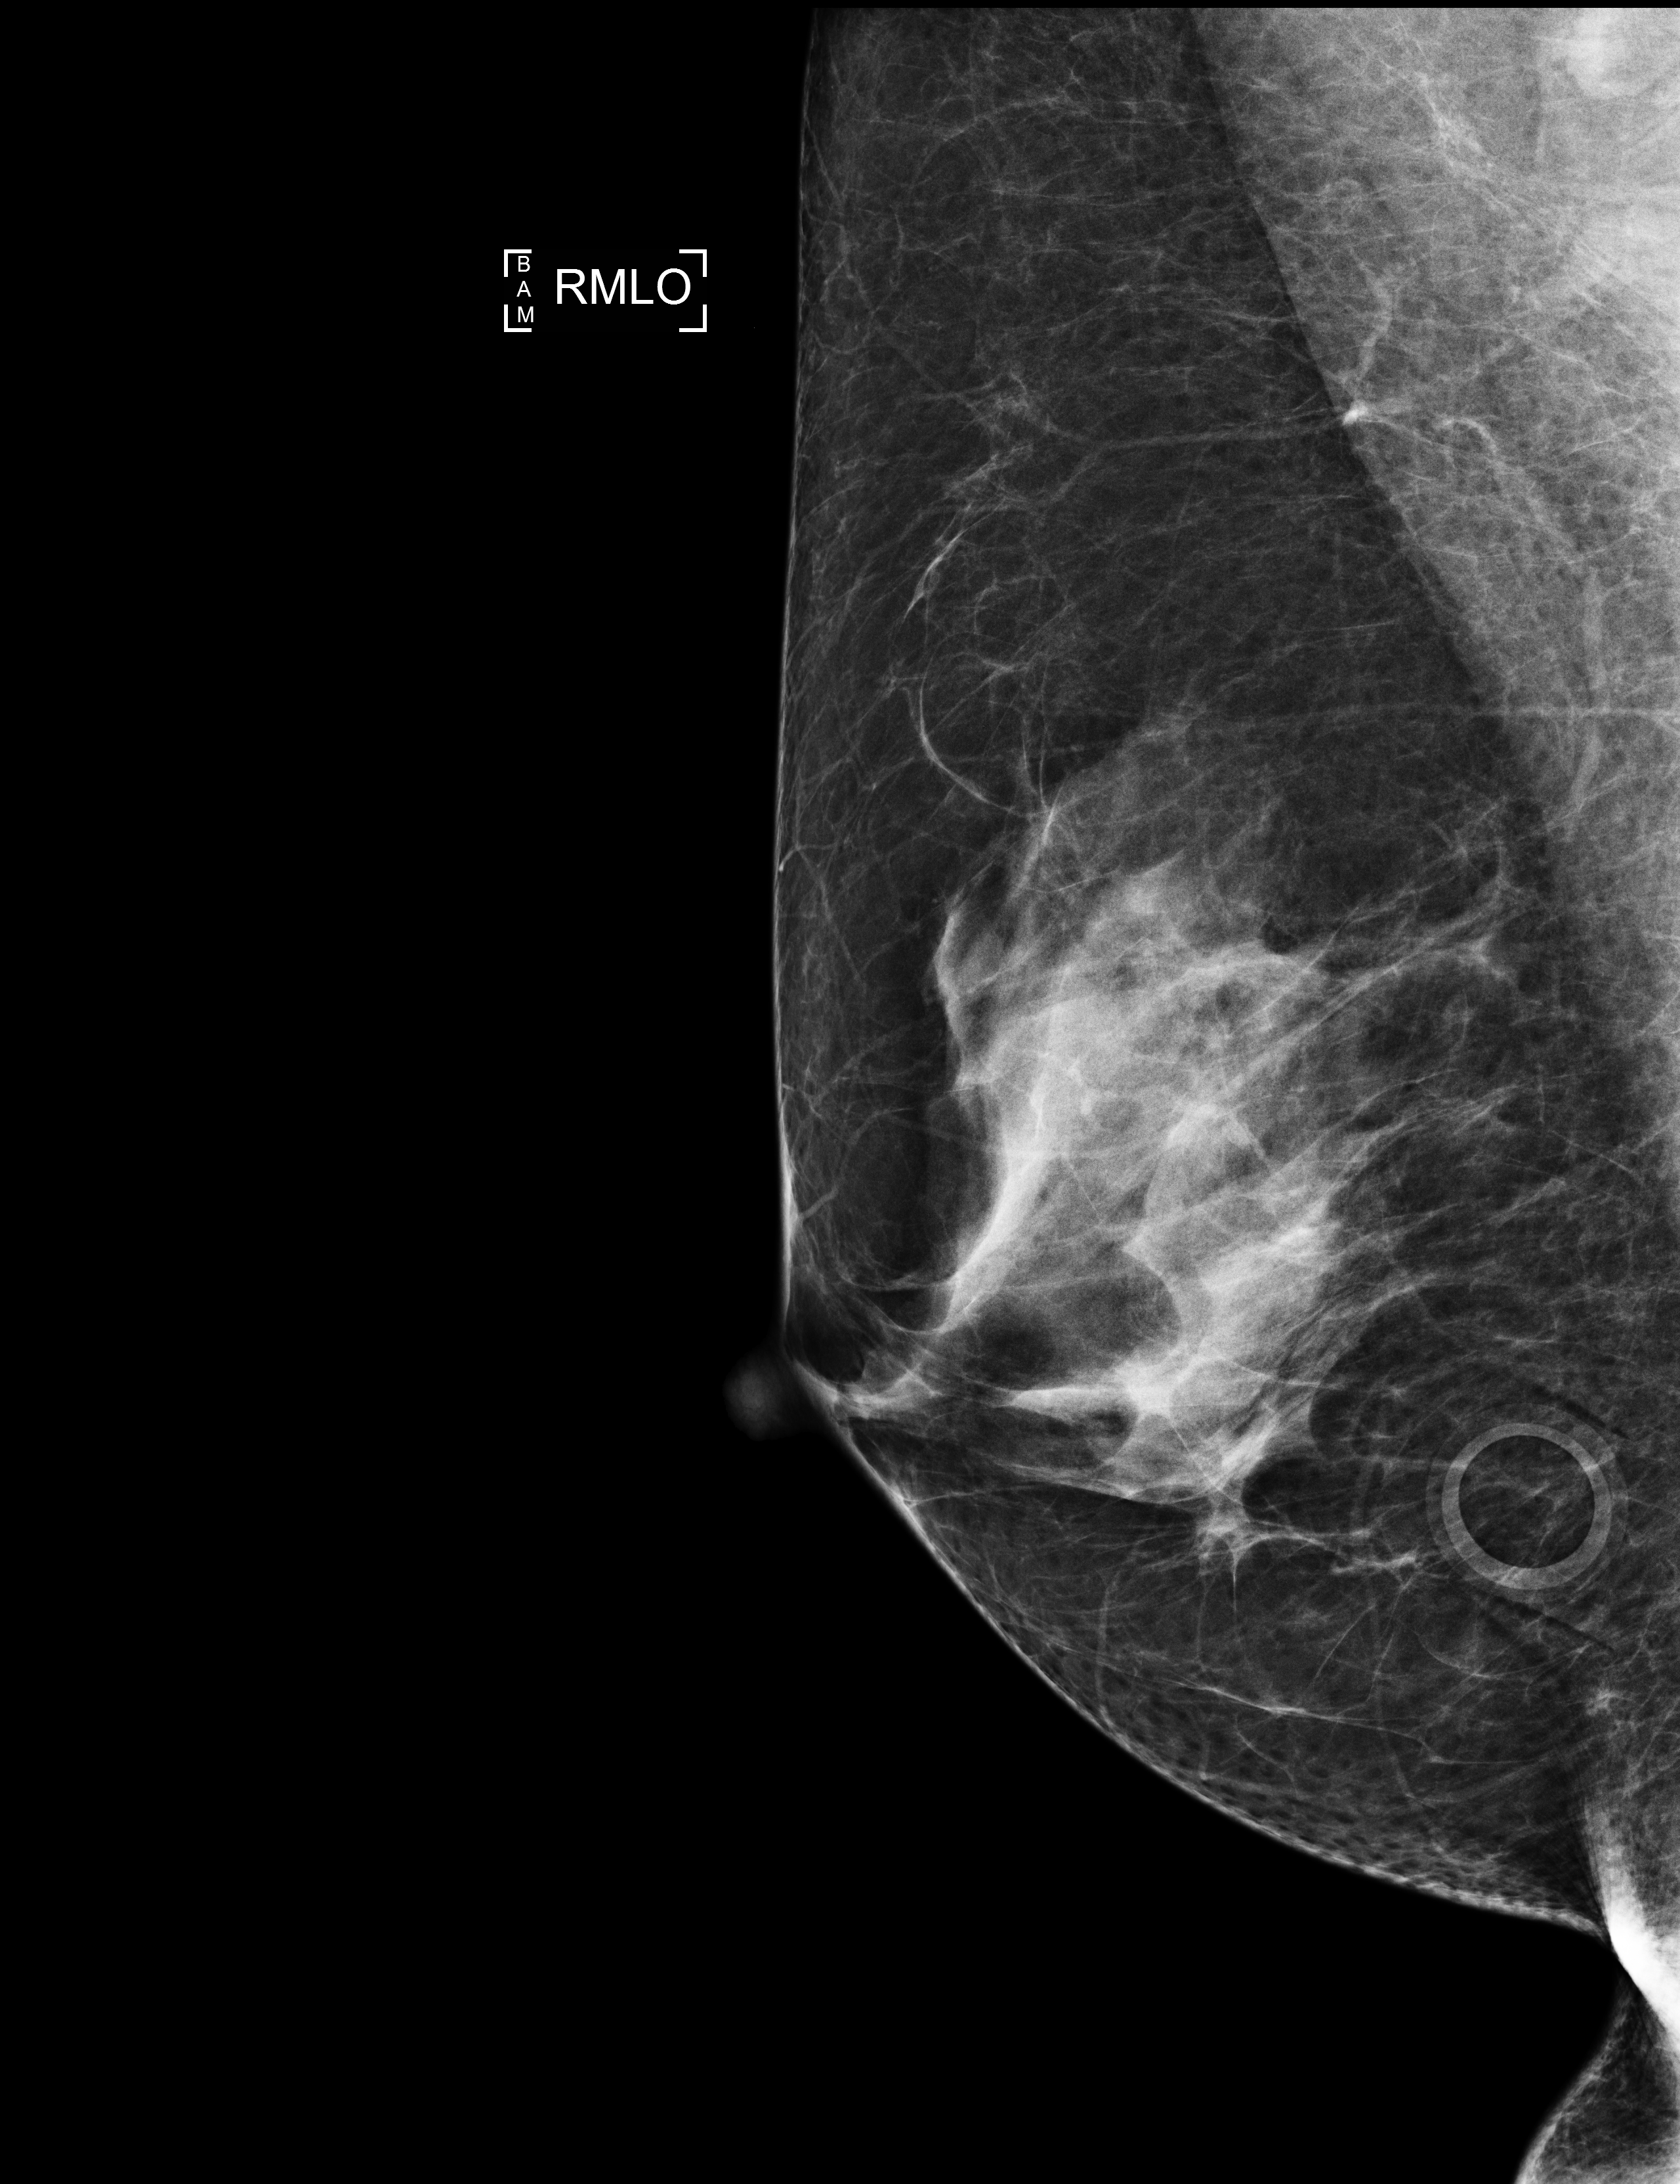
Annual screening mammography examination; system: Selenia Dimensions. Patient aged 60 years (female).
Image type: full-field digital mammogram. Breast: right. Projection: MLO view.